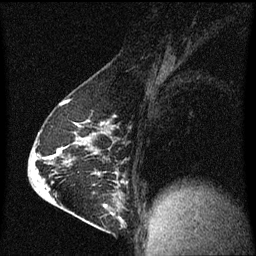
Breast MRI (dynamic contrast-enhanced), one sagittal slice. Dynamic contrast-enhanced series, image 2 of 3 at this slice position (ordered by acquisition). 1.5 T. TE 4.2 ms, TR 8 ms. 2 mm slice thickness. 256 × 256 image matrix, field of view 200 × 200 mm. Female patient, age 63 years.
Structures marked on this image (semi-automatic segmentation, software-assisted and operator-edited):
- analysis volume of interest (the breast-tissue region the enhancement analysis was run in; not a lesion): bounding box (x1, y1, x2, y2) in pixels: (88, 182, 129, 229)
- tumour enhancement mask (voxels above the 70 % enhancement threshold inside the analysis volume of interest): (104, 182, 123, 221)